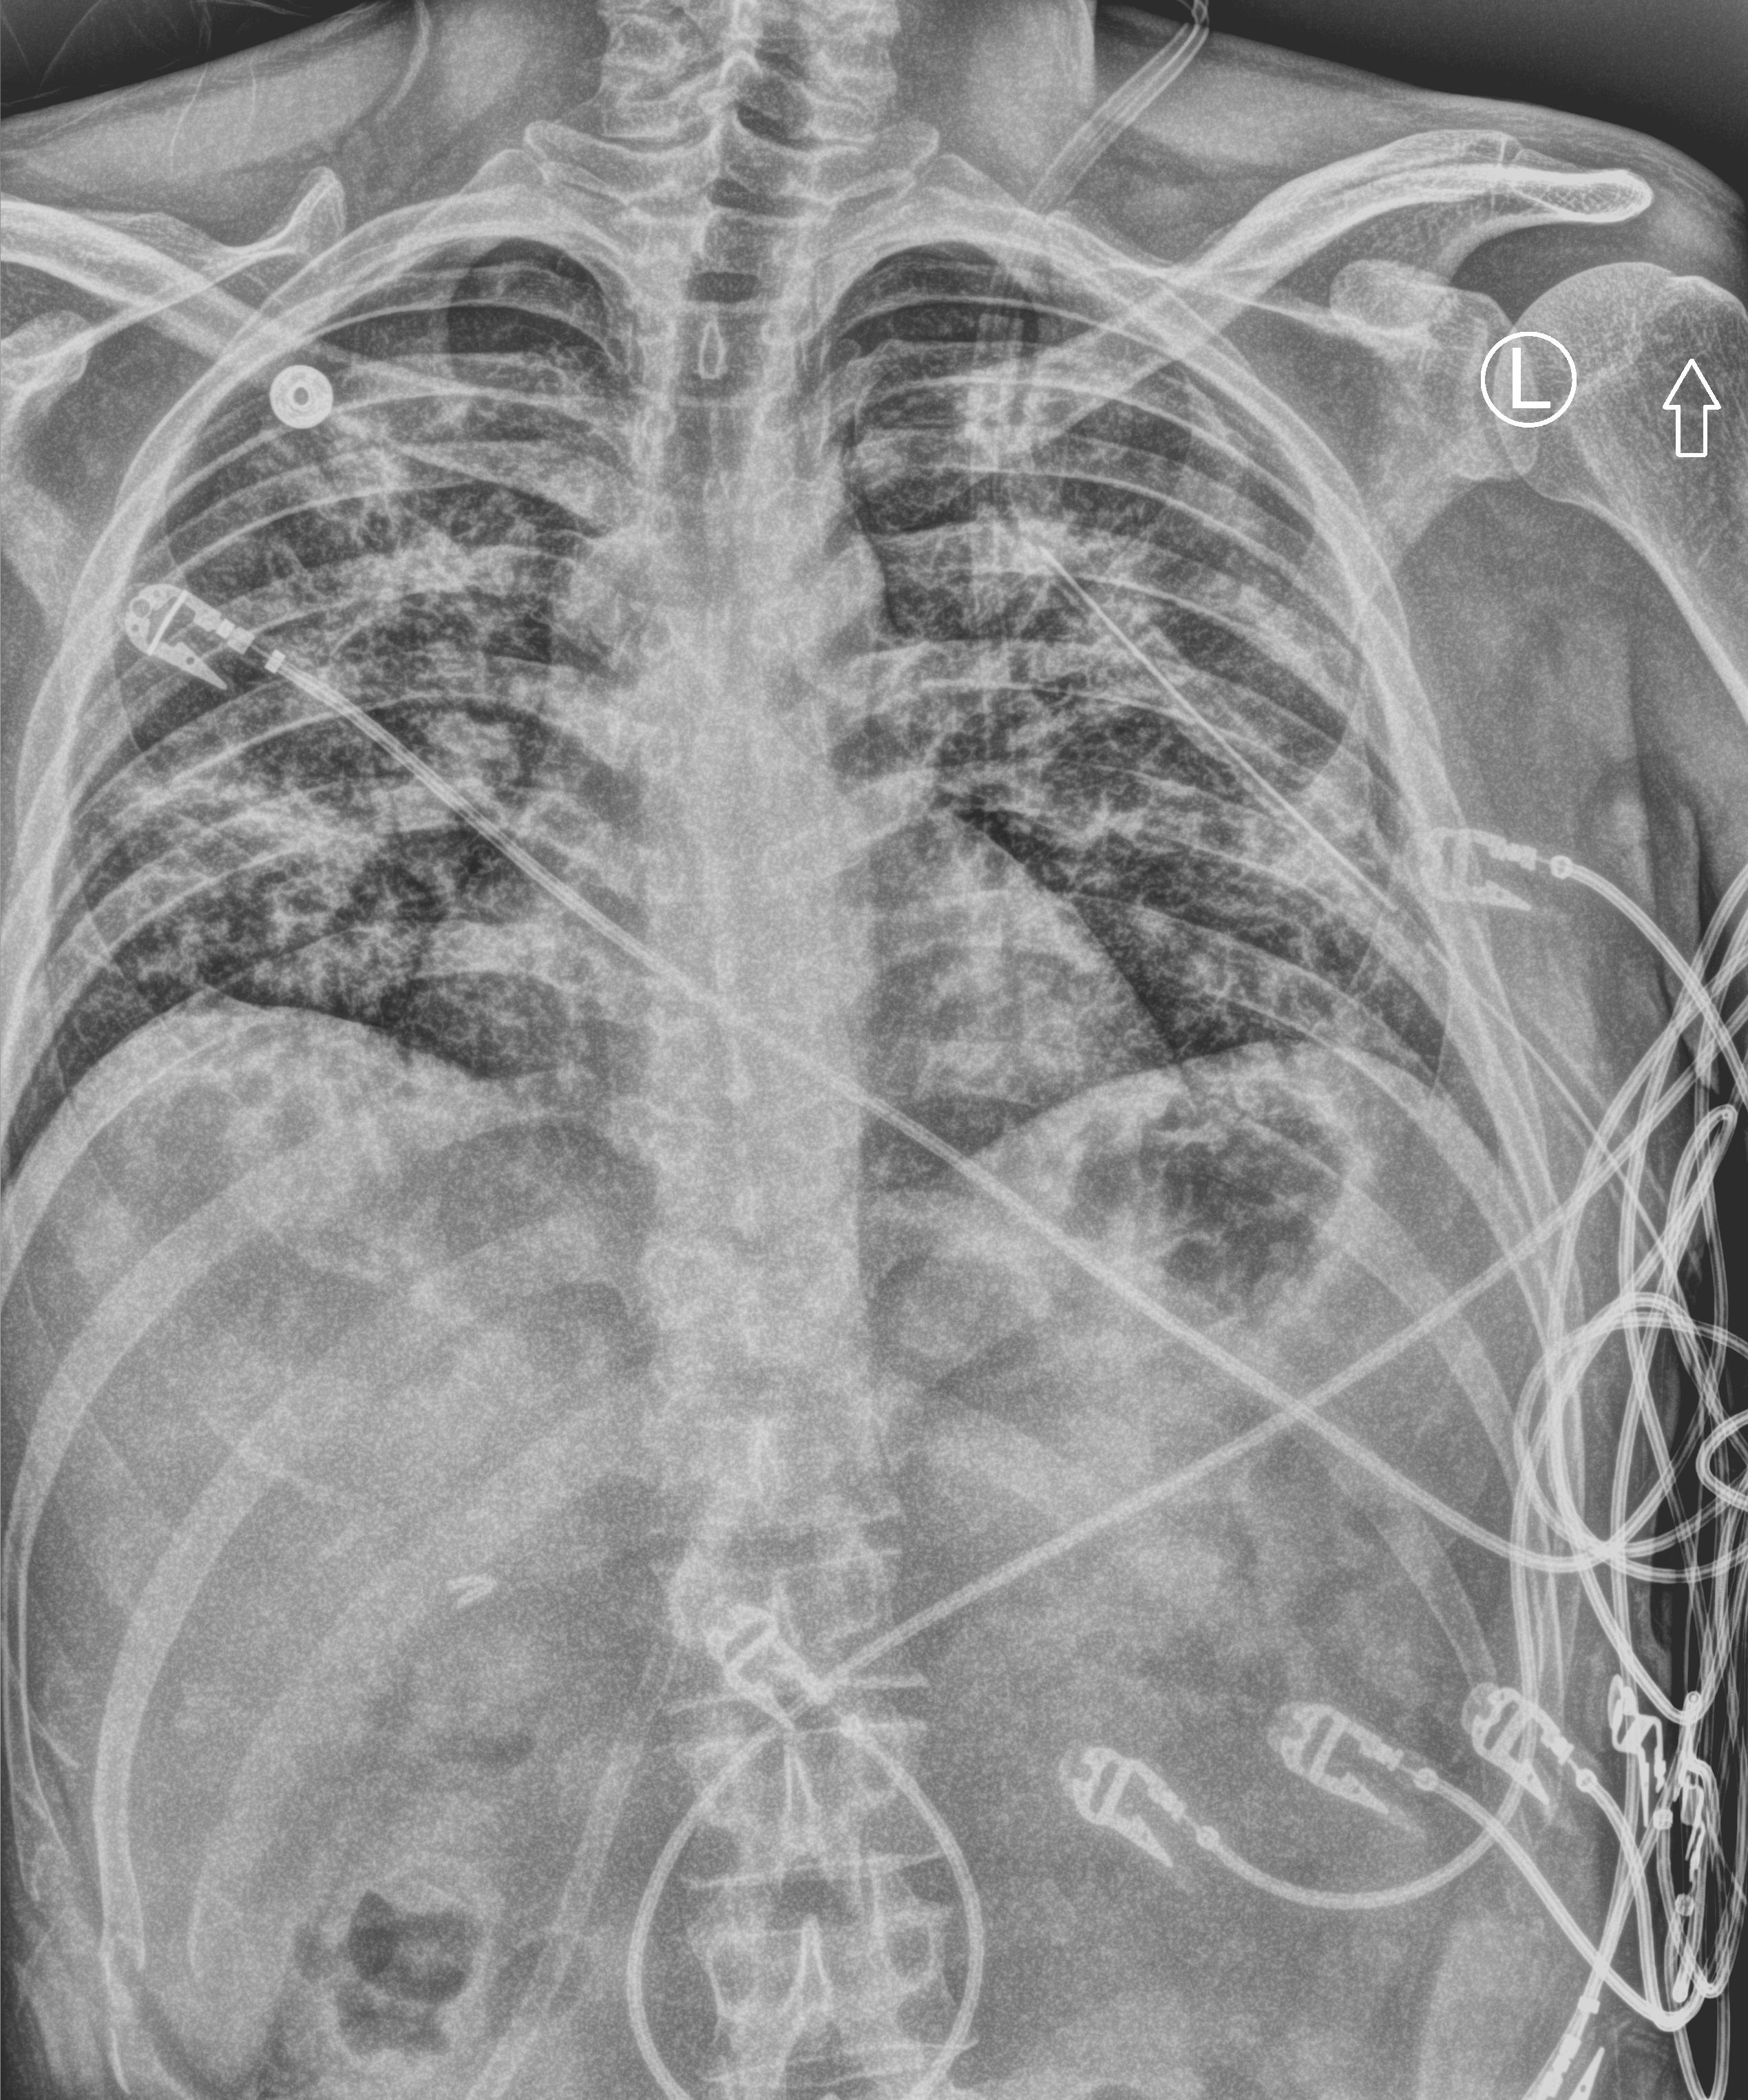
Chest X-ray (portable), anteroposterior (AP) projection. Male patient hospitalised with COVID-19, age 18–59 years.
Hospital-stay facts (about this admission, not read from this image; timing relative to this image not recorded): mechanically ventilated during this hospital stay: yes; admitted to intensive care during this hospital stay: yes.